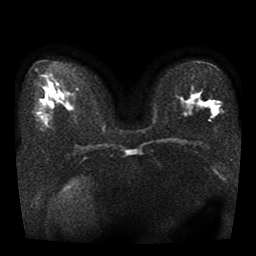
Breast MRI, one axial slice; slice 20 of 41 in the series (ordered by position); diffusion-weighted series; image 2 of 4 stored at this slice position (different b-values; order by instance number); 1.5 T; 5 mm slice thickness; 256 × 256 image matrix, field of view 330 × 330 mm. Female patient.
Annotated regions visible in this slice (manually delineated by an expert):
- tumour on diffusion-weighted imaging: bounding box [x1, y1, x2, y2] px = [210, 102, 218, 110]